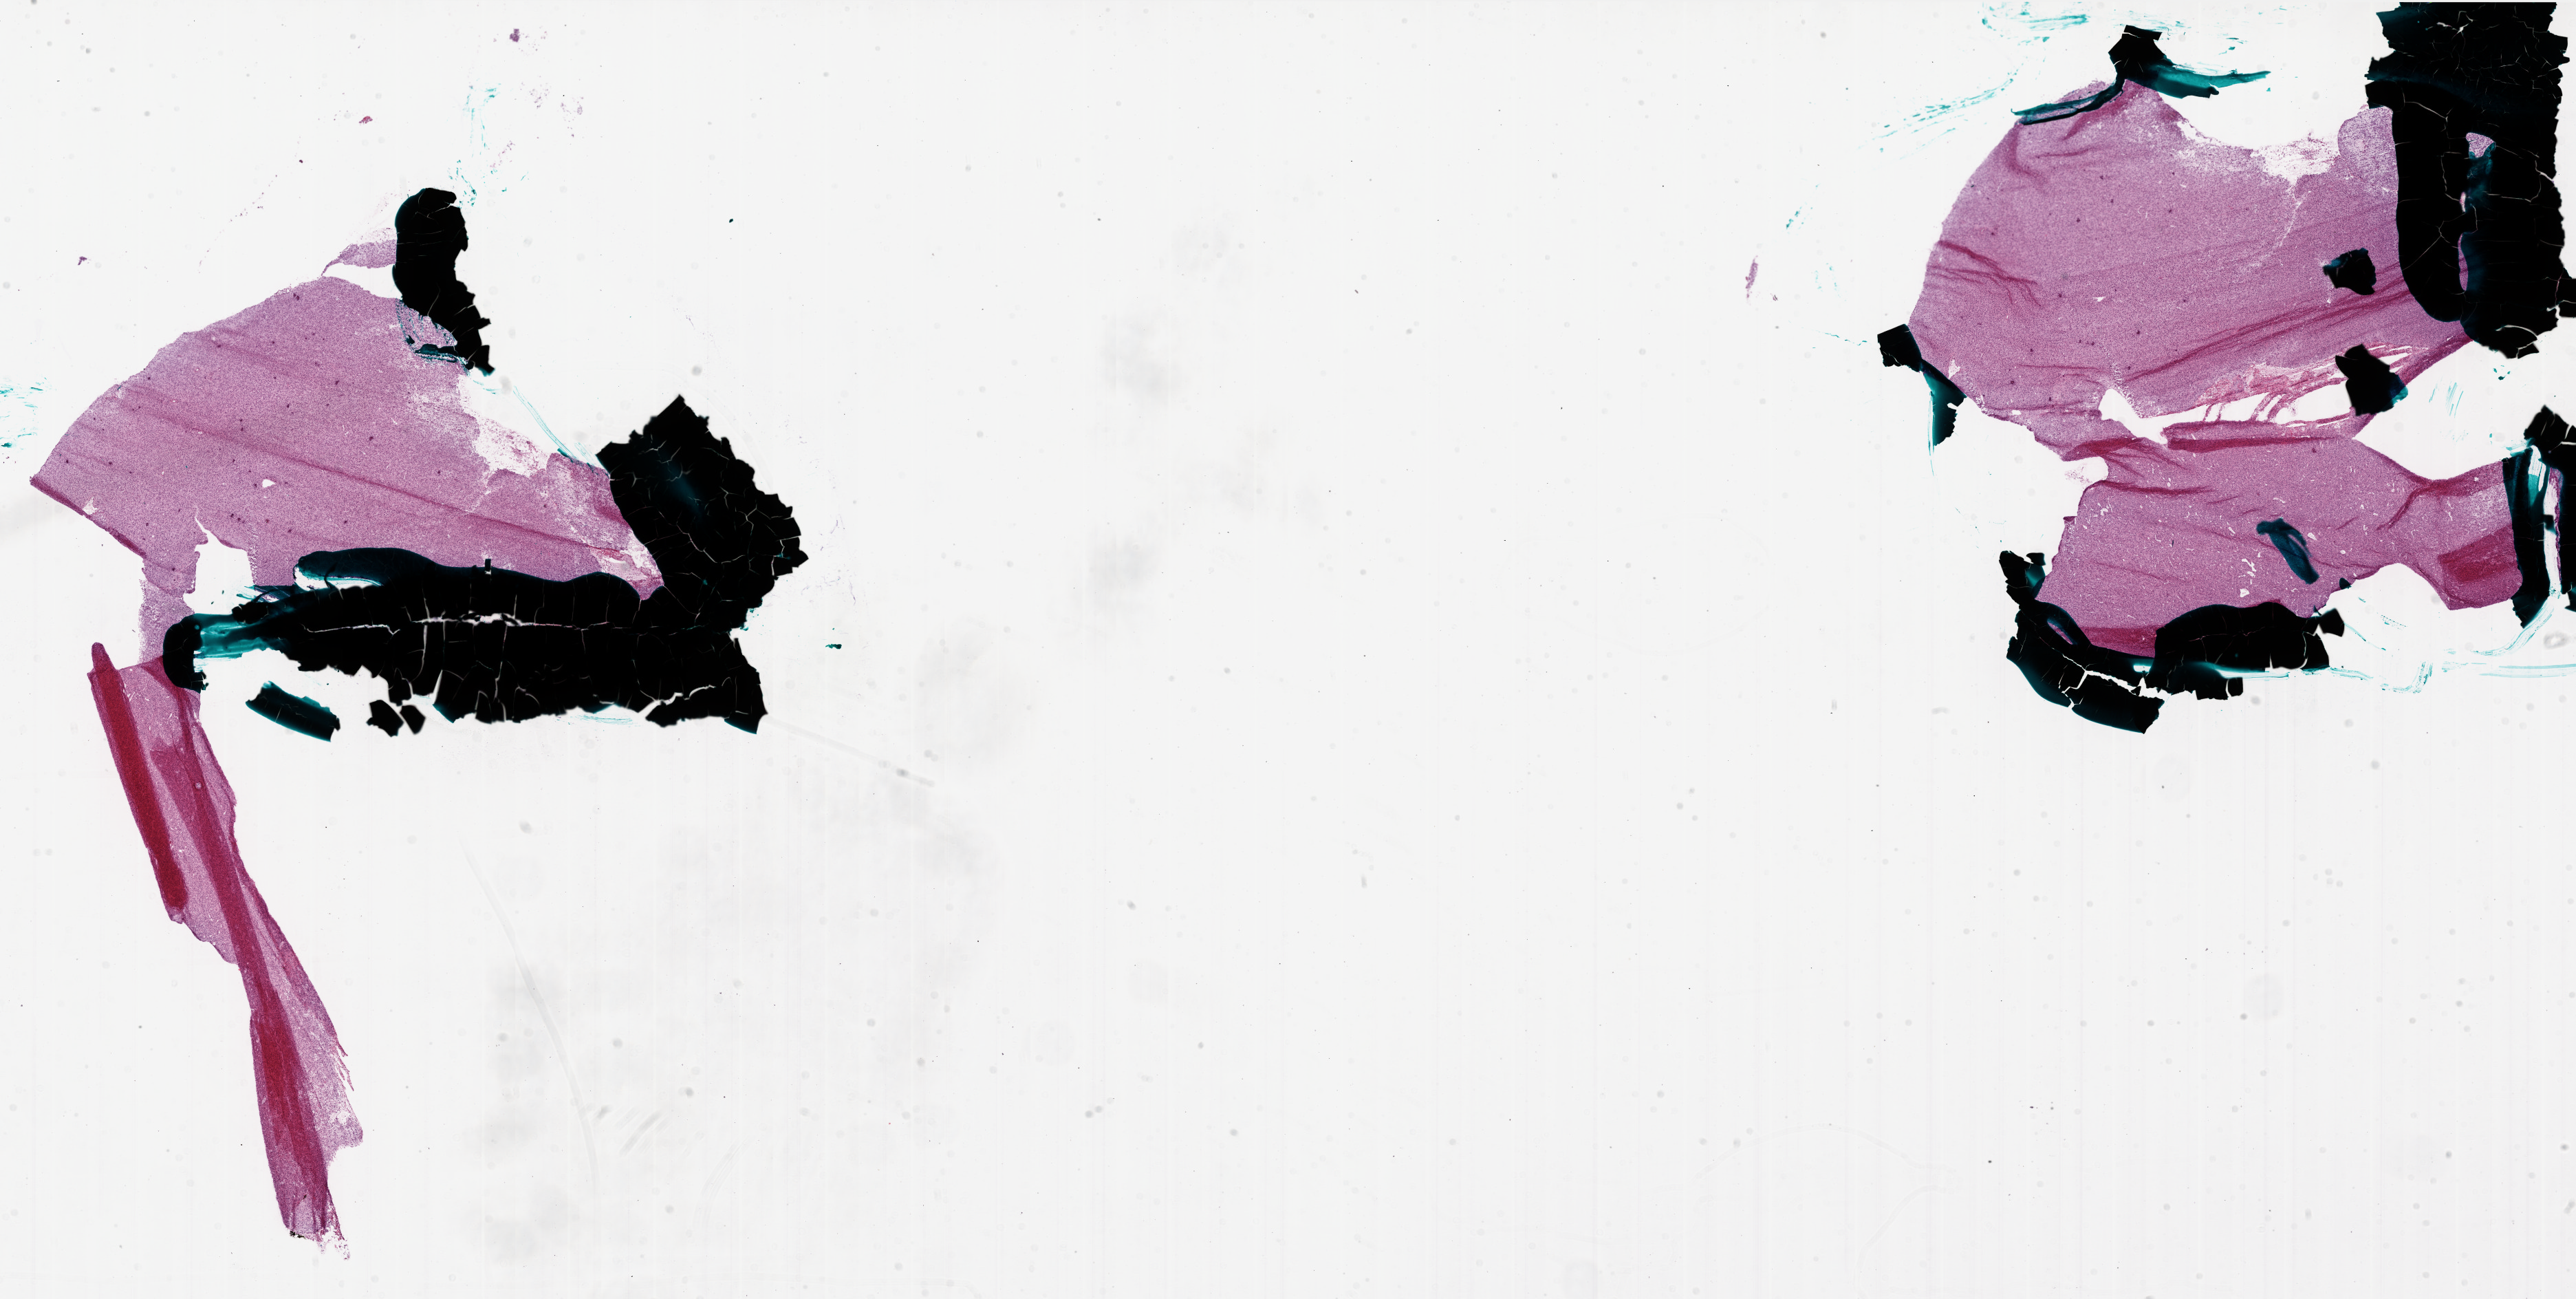
Whole-slide histology image, H&E-stained, a low-resolution overview of the entire scanned area, about 30.0 x 15.1 mm, frozen section, sample: primary tumour, brain. Female, age 53 years at initial diagnosis. Composition of this section per pathologist review: tumour cells 95%, tumour nuclei 100%, normal cells 0%, stromal cells 0%, necrosis 5%. Inflammatory infiltration, as recorded: lymphocyte infiltration 0%, monocyte infiltration 0%, neutrophil infiltration 0%.
Diagnosis: Glioblastoma.